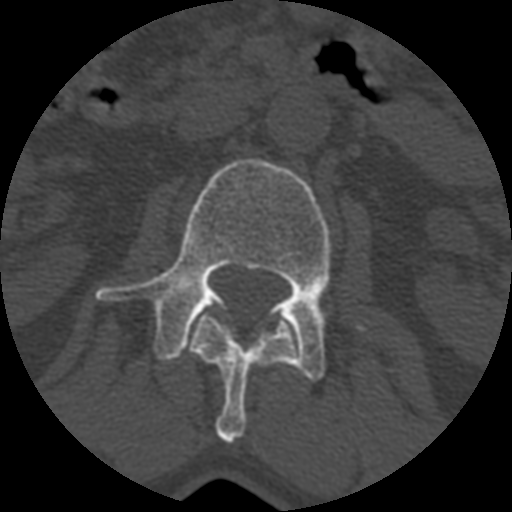
CT including the spine, one axial slice. Position 342 of 399 along the scan axis. Bone window (W 1800 / L 400 HU). 1.25 mm slice thickness. 512 × 512 image matrix, field of view 160 × 160 mm. Patient age 71 years. From the clinical record (not read from this slice): primary cancer: prostate.
Structures marked on this image (semi-automatic segmentation, software-assisted and operator-edited):
- L1 vertebra: bounding box [x1, y1, x2, y2] px = [187, 308, 296, 444]
- L2 vertebra: [95, 159, 365, 380]